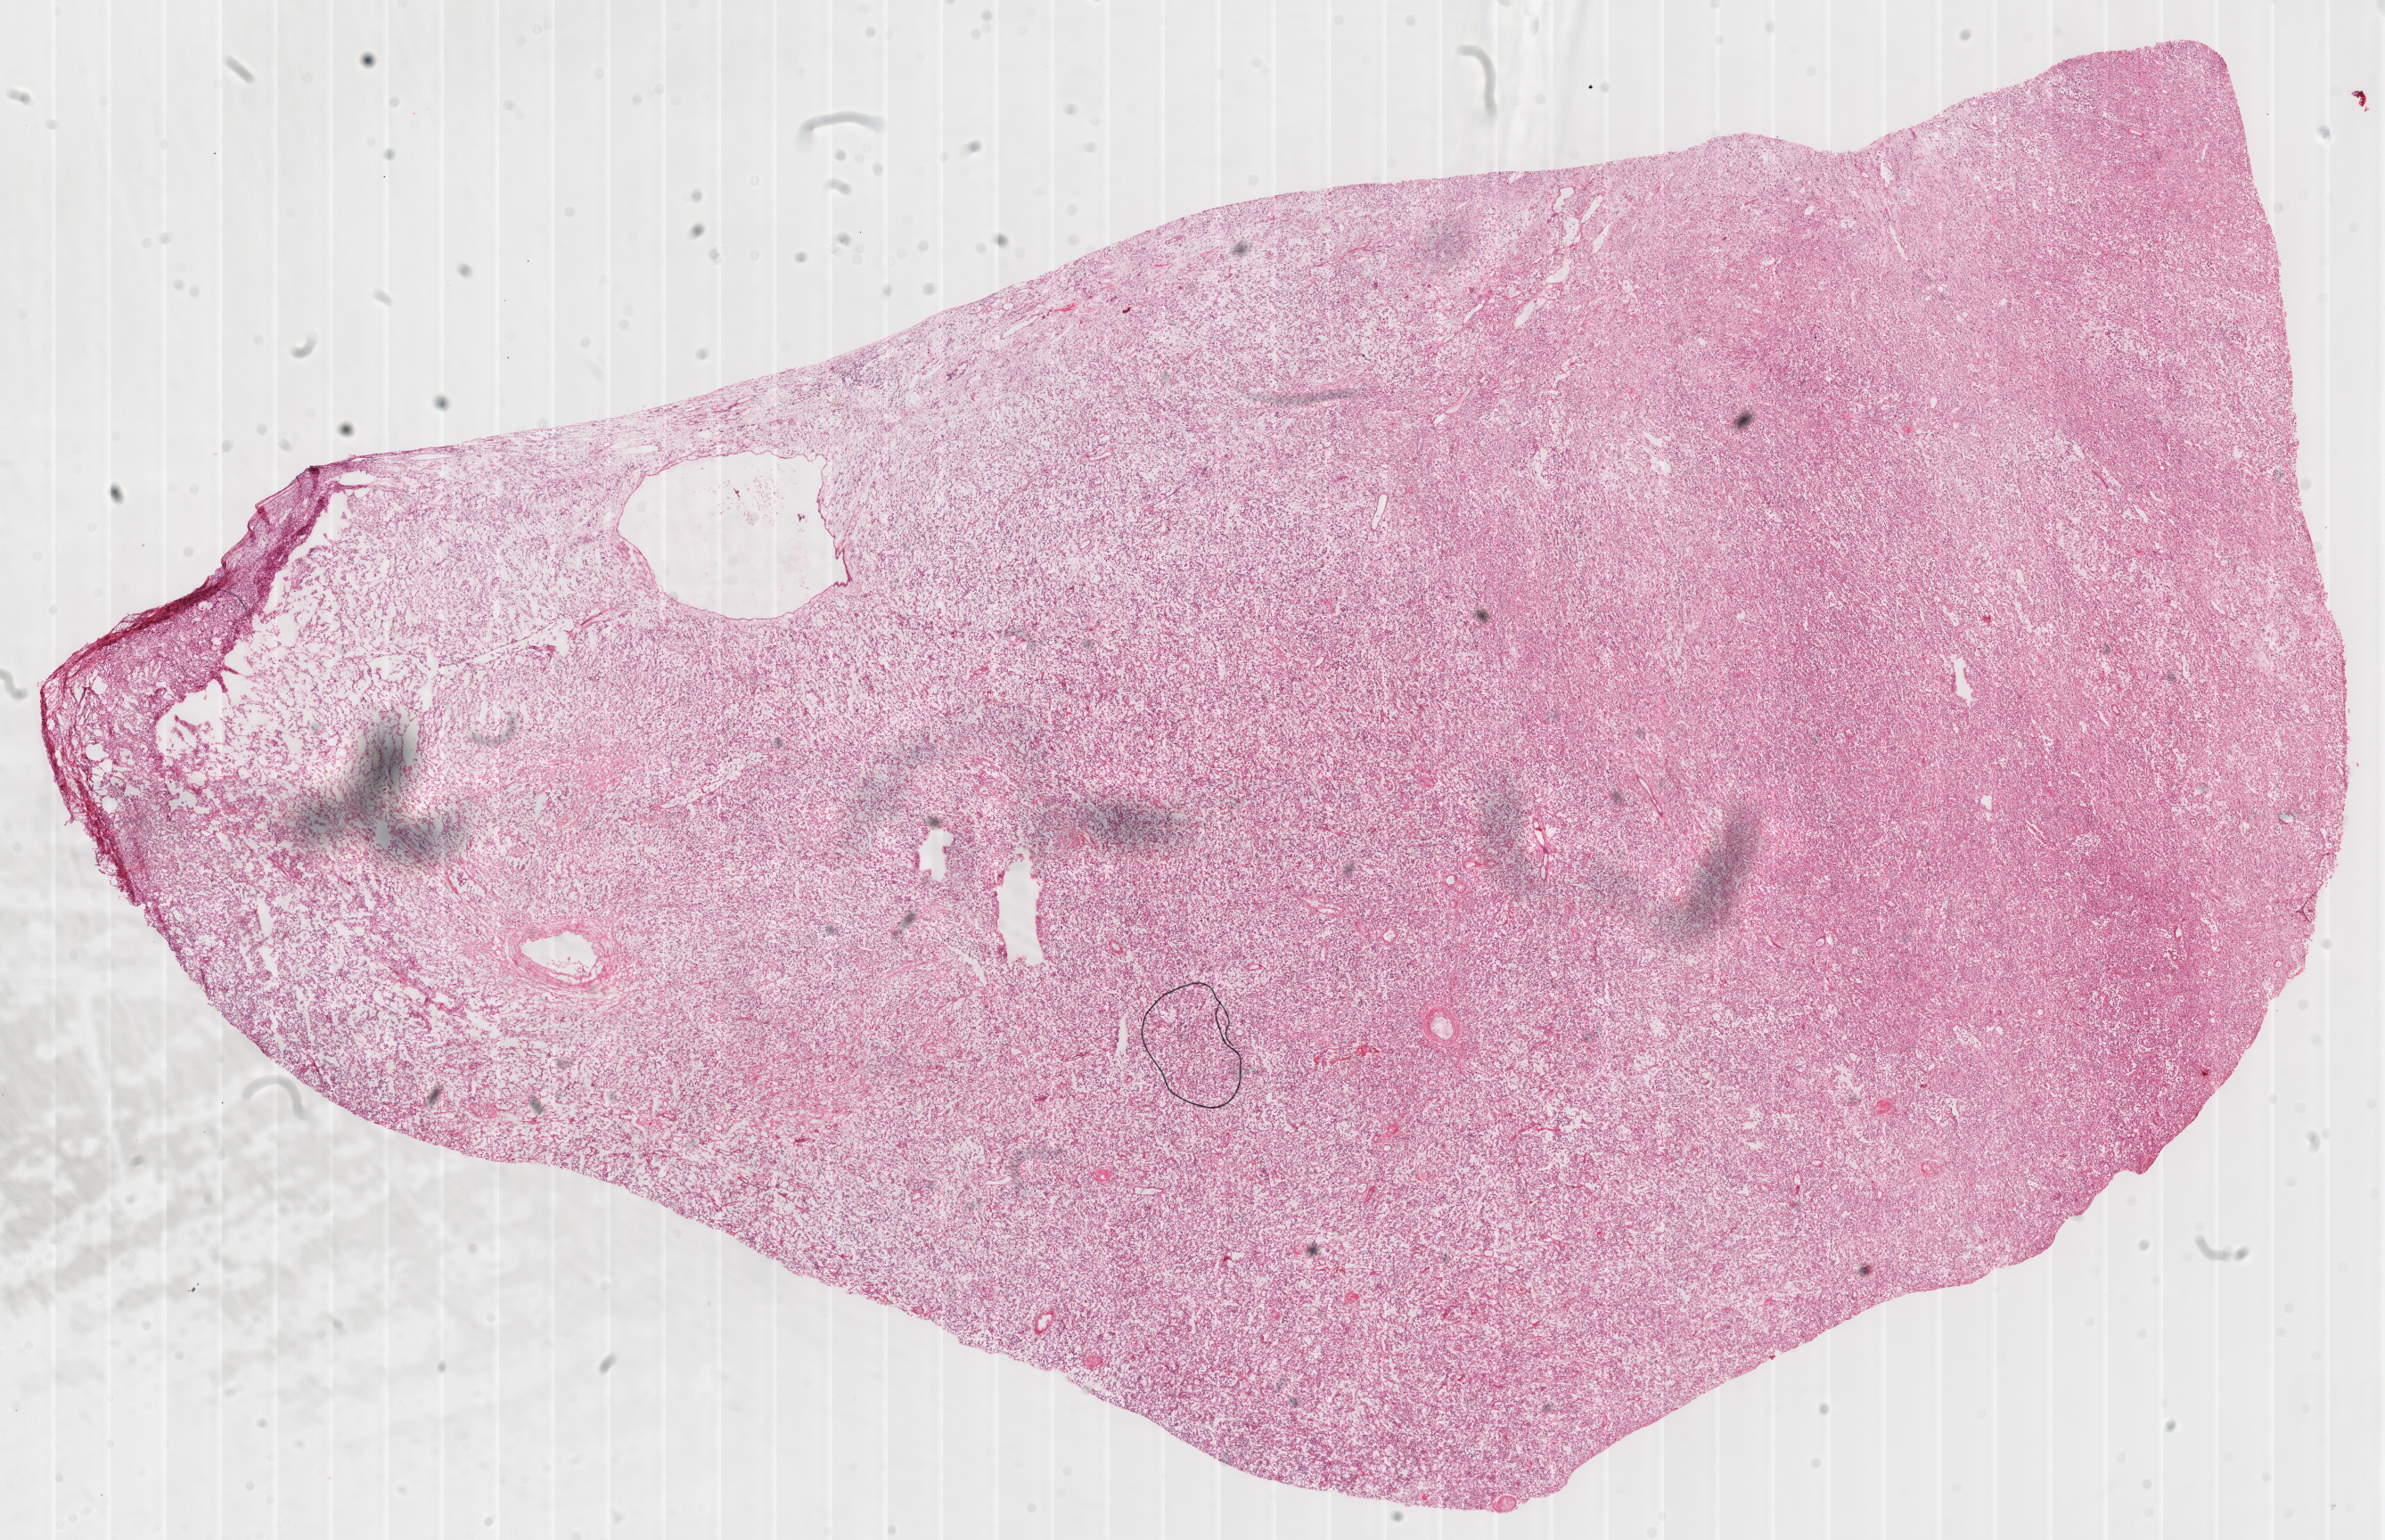
Digitized H&E-stained tissue section (whole slide), whole scanned area (about 21.0 x 13.6 mm) shown as a low-resolution overview, frozen section from the top of the tissue portion, sample: primary tumour, kidney. Male patient; age at initial diagnosis 54 years. Slide review estimates, as recorded: tumour cells 100%, tumour nuclei 95%, normal cells 0%, stromal cells 0%, necrosis 0%. Infiltration values recorded for this section: lymphocyte infiltration 0%, monocyte infiltration 0%, neutrophil infiltration 0%.
* TNM: T4 N1
* laterality: left
* diagnosis: Renal cell carcinoma, chromophobe type
* AJCC pathologic stage: IV
* lymph nodes positive (case pathology): 1 of 4 examined